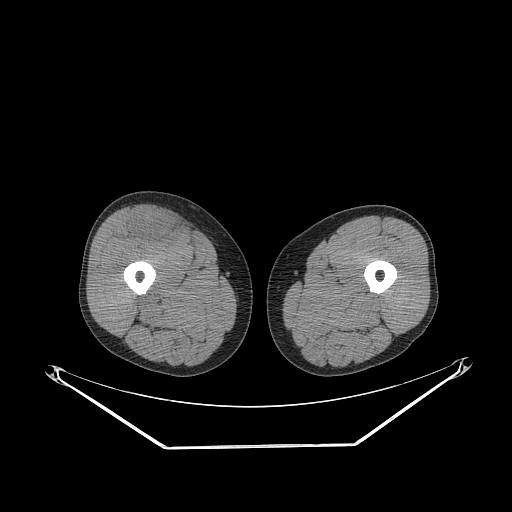
CT of an extremity soft-tissue mass (from a PET/CT study), one axial slice; slice 262 of 311 in the series (ordered by position); reconstruction kernel STANDARD; soft-tissue window (W 400 / L 40 HU); 3.75 mm slice thickness; 512 × 512 image matrix. Male patient. Case-level facts recorded for this patient, not image findings: histological type: pleiomorphic leiomyosarcoma; grade: intermediate; site of the primary tumour: right thigh.
Structures marked on this image (expert contour drawn on MRI and transferred to this co-registered scan by the dataset authors):
- gross tumour volume including surrounding oedema: bounding box (x1, y1, x2, y2) in pixels: (130, 210, 179, 243)